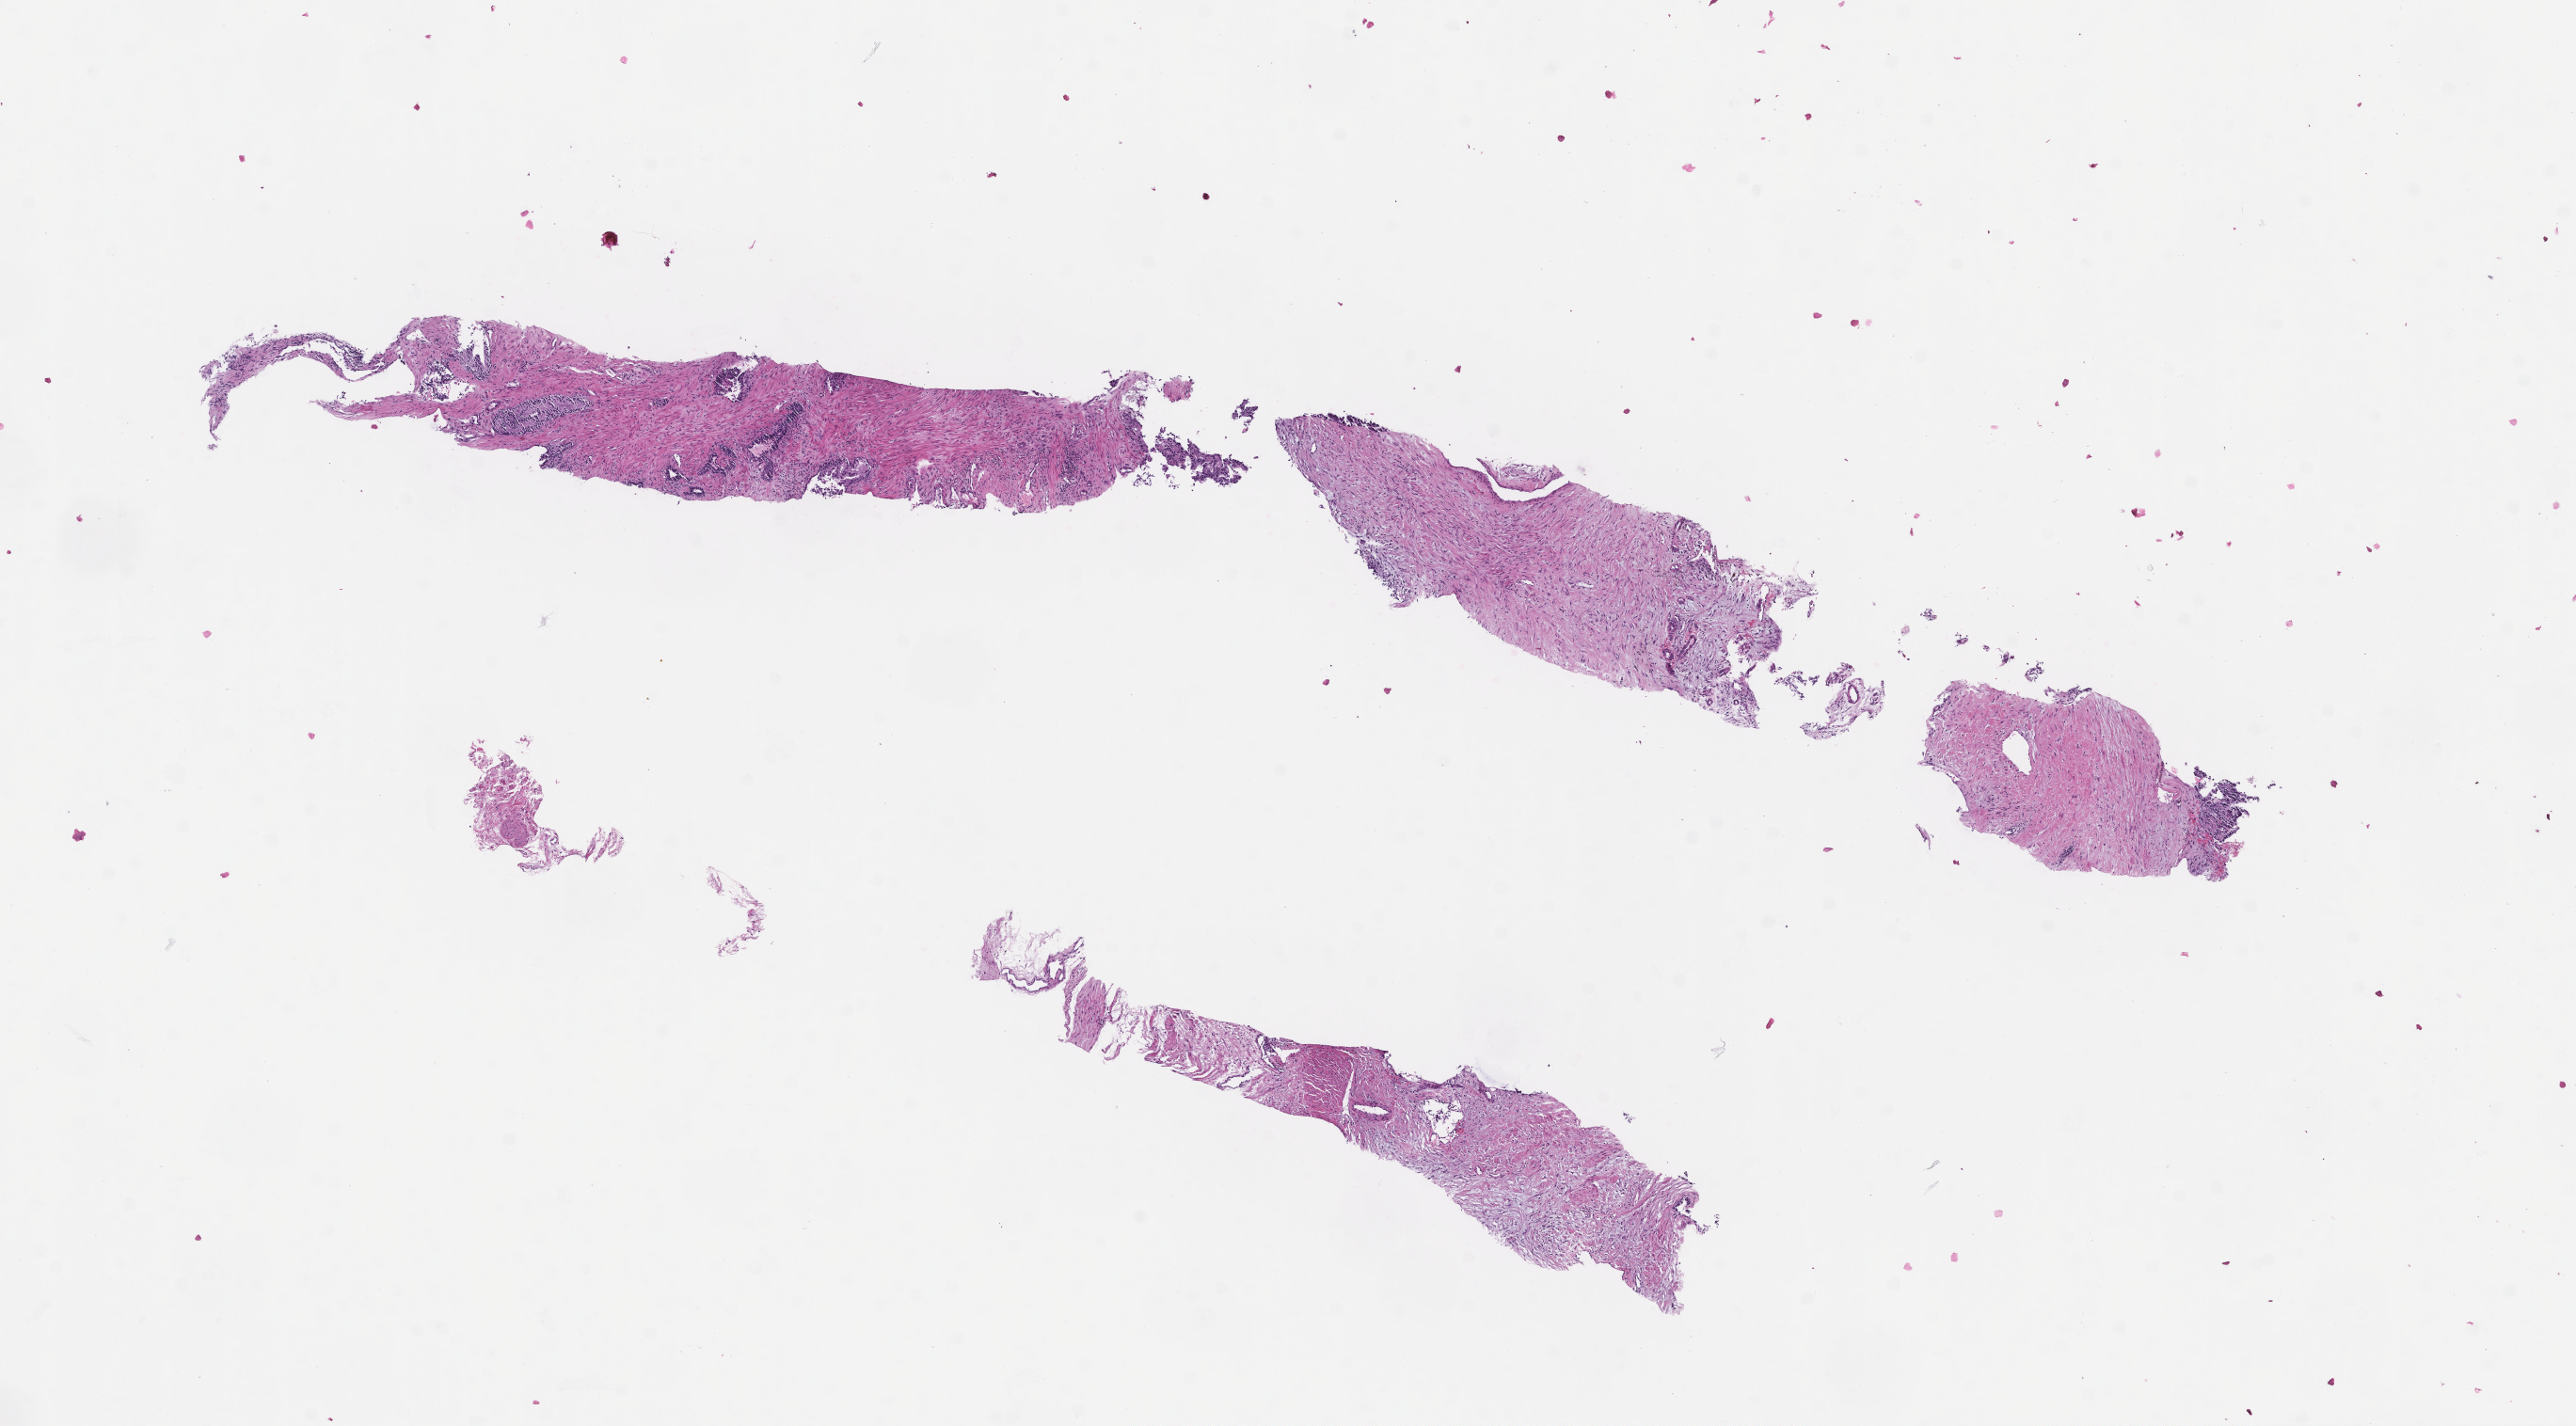
Digitized hematoxylin and eosin (H&E)-stained section, low-resolution overview of the scanned area, about 11.1 x 6.1 mm. FFPE section. Site: prostate. Specimen time point: archival tissue. Patient sex: male.
* this section: primary tumour tissue
* diagnosis: Prostate Carcinoma